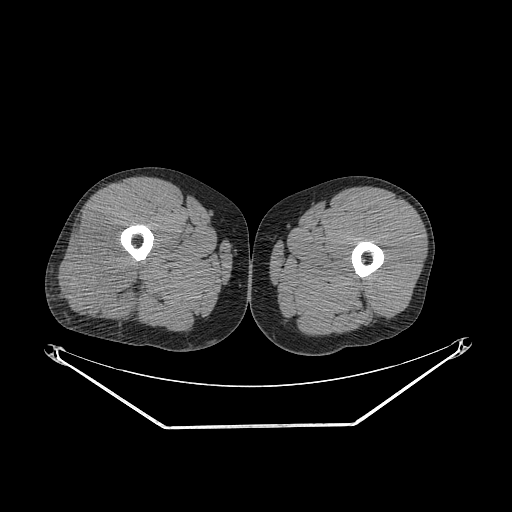
CT of an extremity soft-tissue mass (from a PET/CT study), one axial slice. Slice 250 of 267 in the series (ordered by position). Soft-tissue window (W 400 / L 40 HU). 512 × 512 image matrix, field of view 500 × 500 mm. Male patient. From the clinical record (not read from this slice): histological type: poorly differentiated synovial sarcoma; grade: high; site of the primary tumour: right buttock.
Annotated regions visible in this slice (expert contour drawn on MRI and transferred to this co-registered scan by the dataset authors):
- gross tumour volume including surrounding oedema: box from (x=60, y=219) to (x=147, y=318) px
- gross tumour volume (mass): (x=60, y=221)–(x=143, y=318)